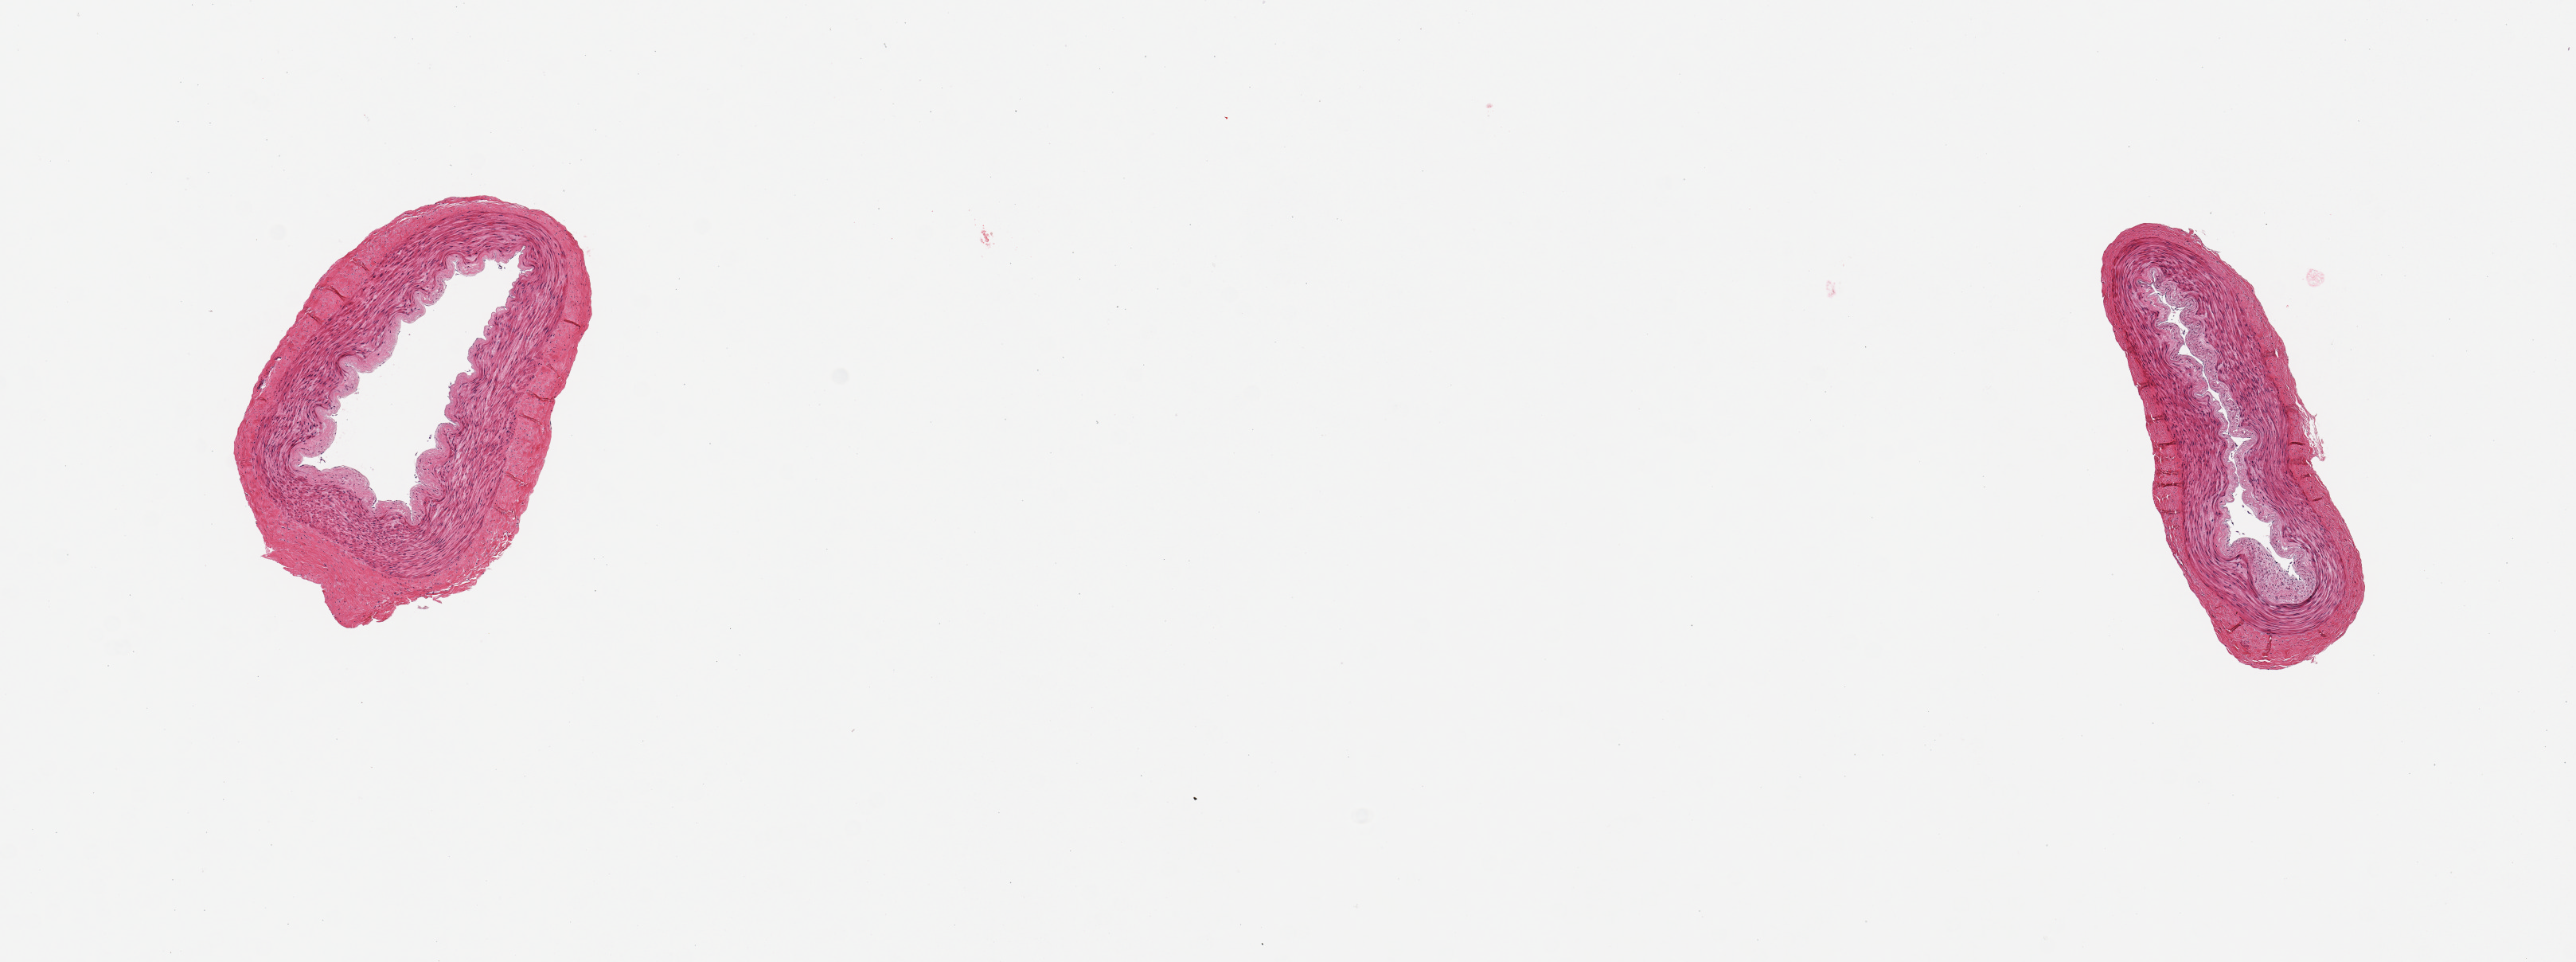
Hematoxylin and eosin (H&E) whole-slide image — low-resolution overview of the scanned area, about 12.8 x 4.8 mm (slide scanned at 20x), PAXgene-fixed, paraffin-embedded tissue, section of tibial artery (target tissue), tissue donor sample. Female donor.
- review note (as recorded): 2 pieces; well trimmed; no lesions